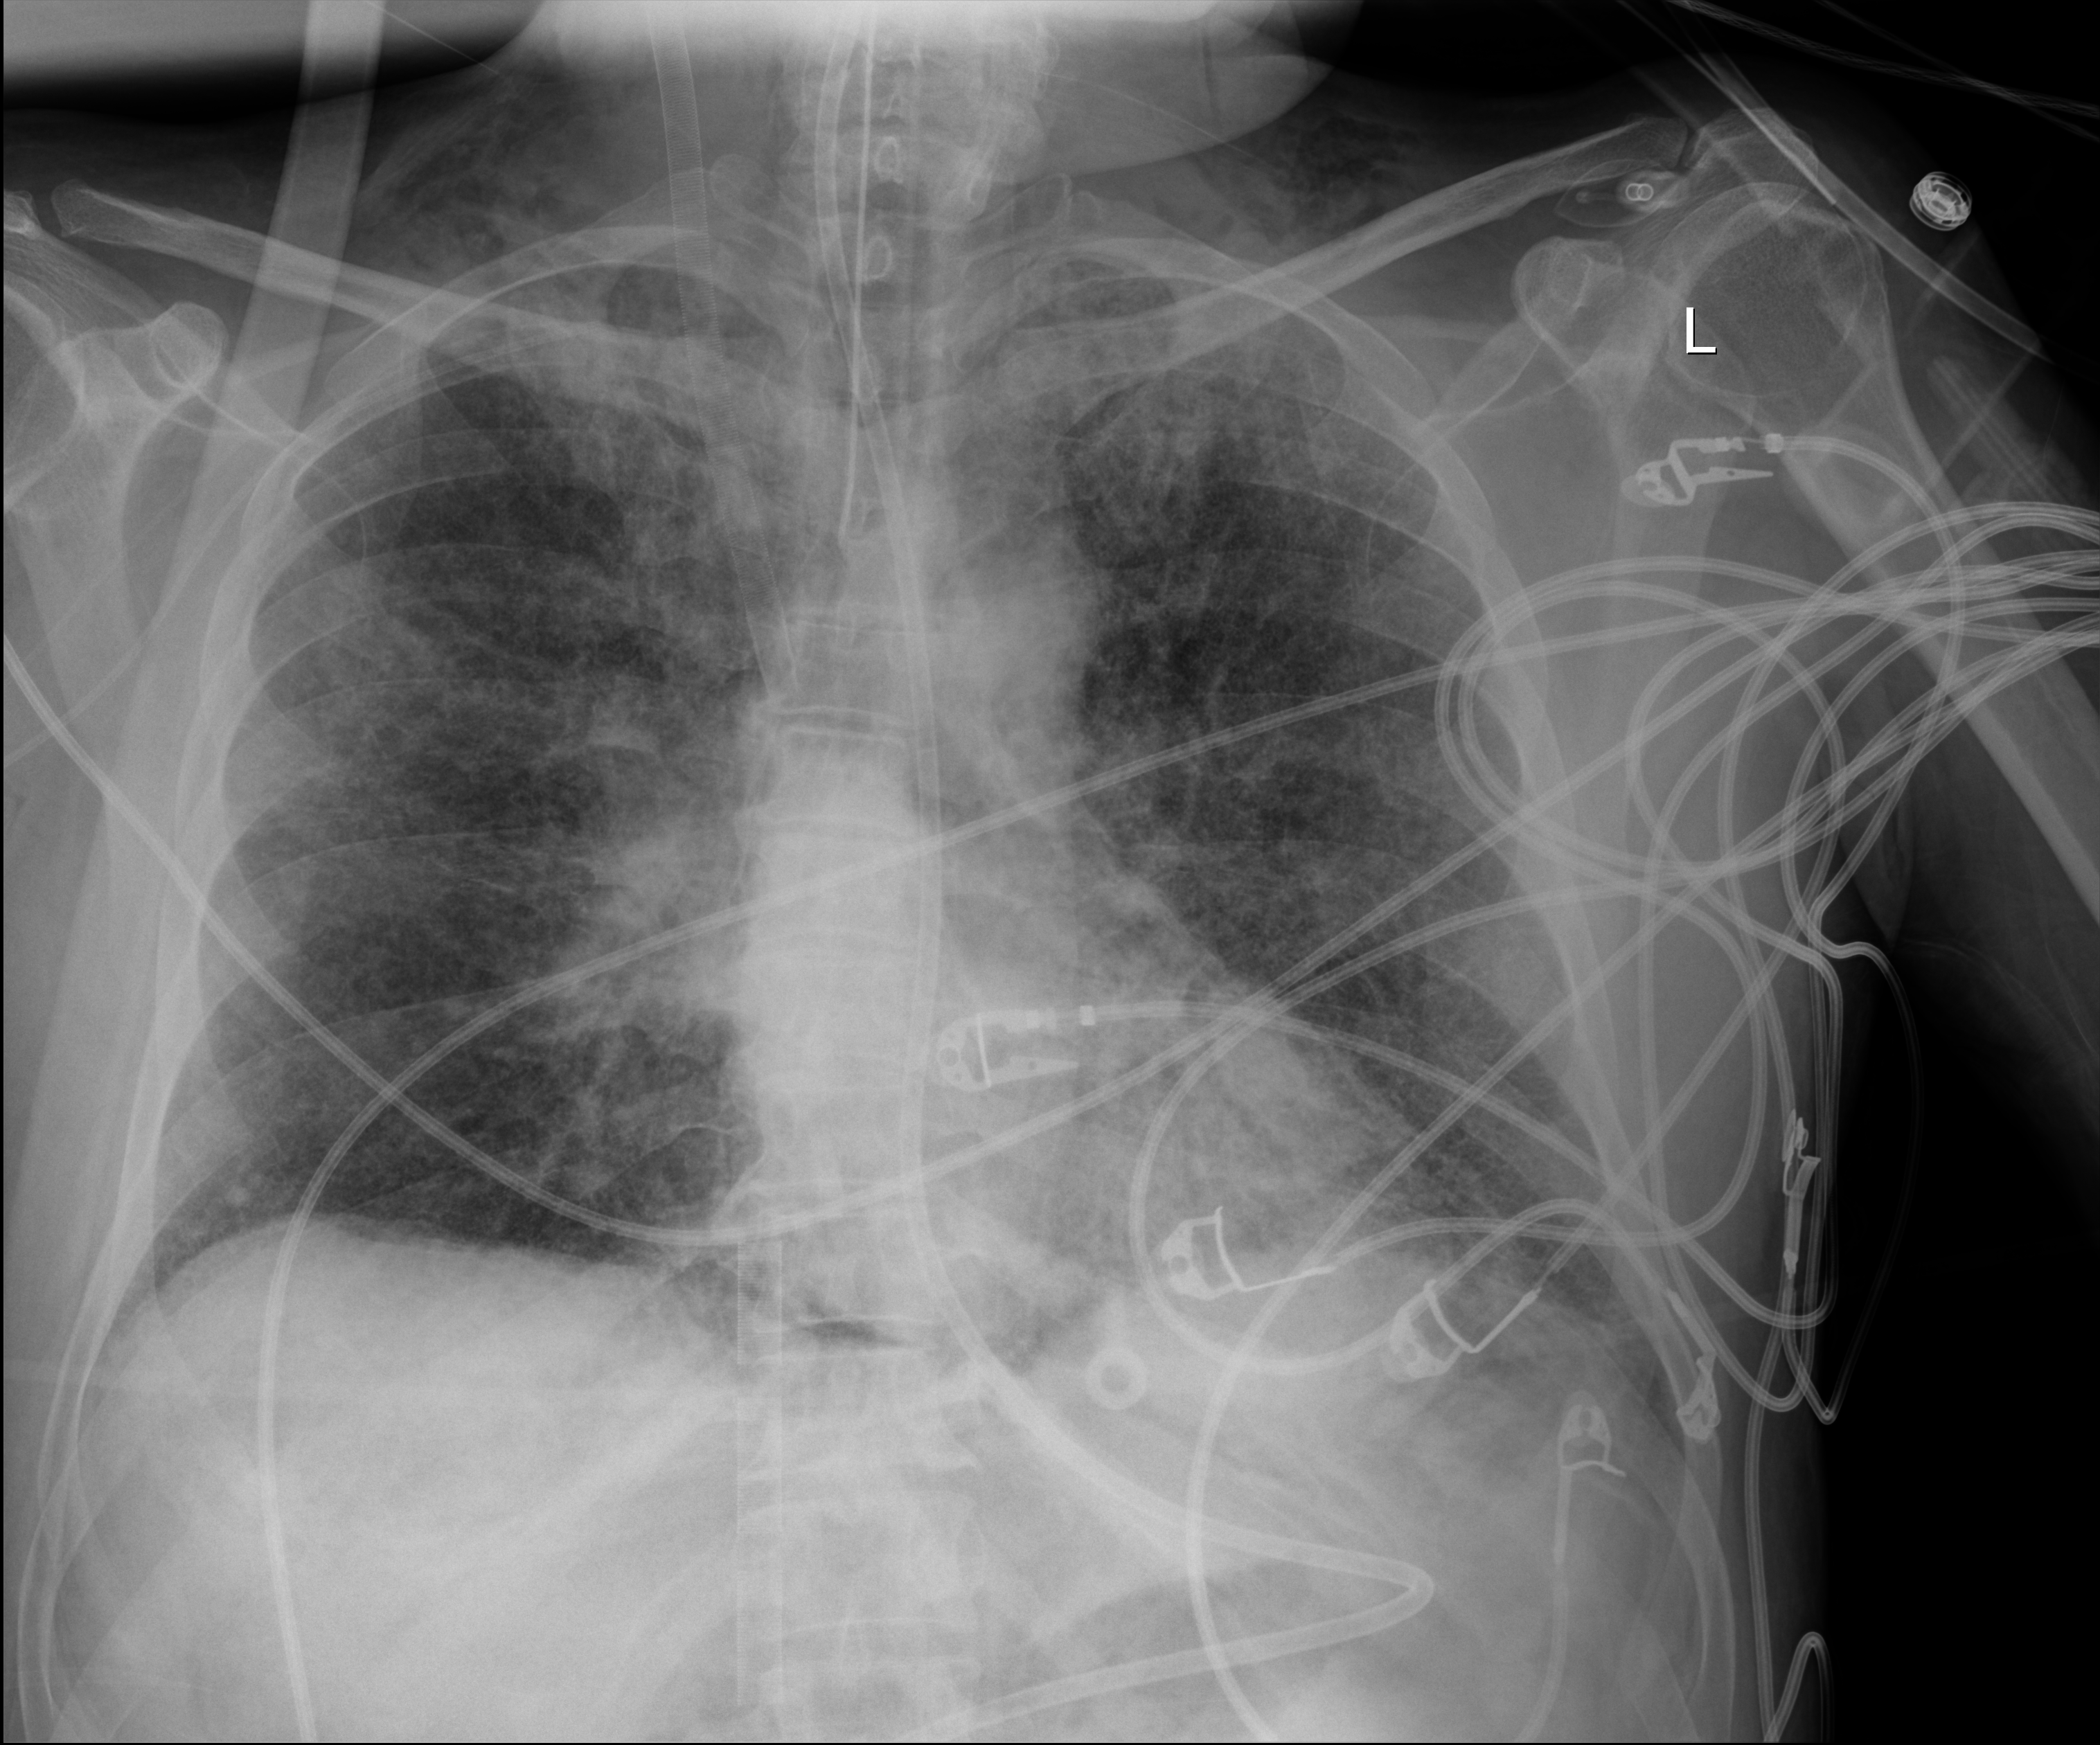
Chest radiograph (digital radiography); anteroposterior (AP) projection. Patient hospitalised with COVID-19; male, aged 18–59 years.
Admission-level facts for this patient (not findings on this image; timing relative to this image not recorded):
- smoking status (admission record): never